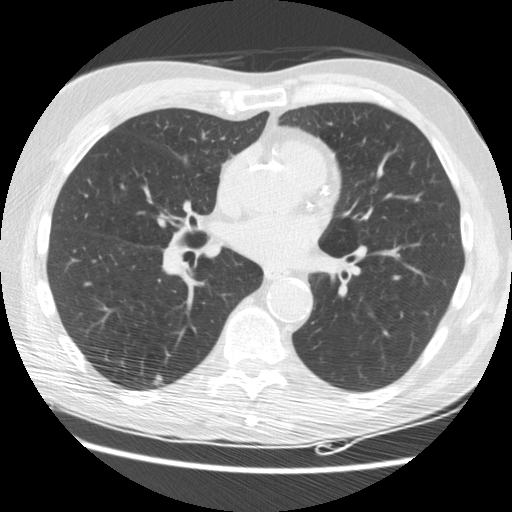
Low-dose screening chest CT, one axial slice. Position 84 of 176 along the scan axis. Reconstruction kernel STANDARD. Lung window (W 1500 / L -600 HU). 512 × 512 image matrix, field of view 347 × 347 mm.
Annotated regions visible in this slice (expert manual segmentation):
- lesion 2 (tumor, lower lobe of right lung): bounding box (x1, y1, x2, y2) in pixels: (151, 373, 163, 386)